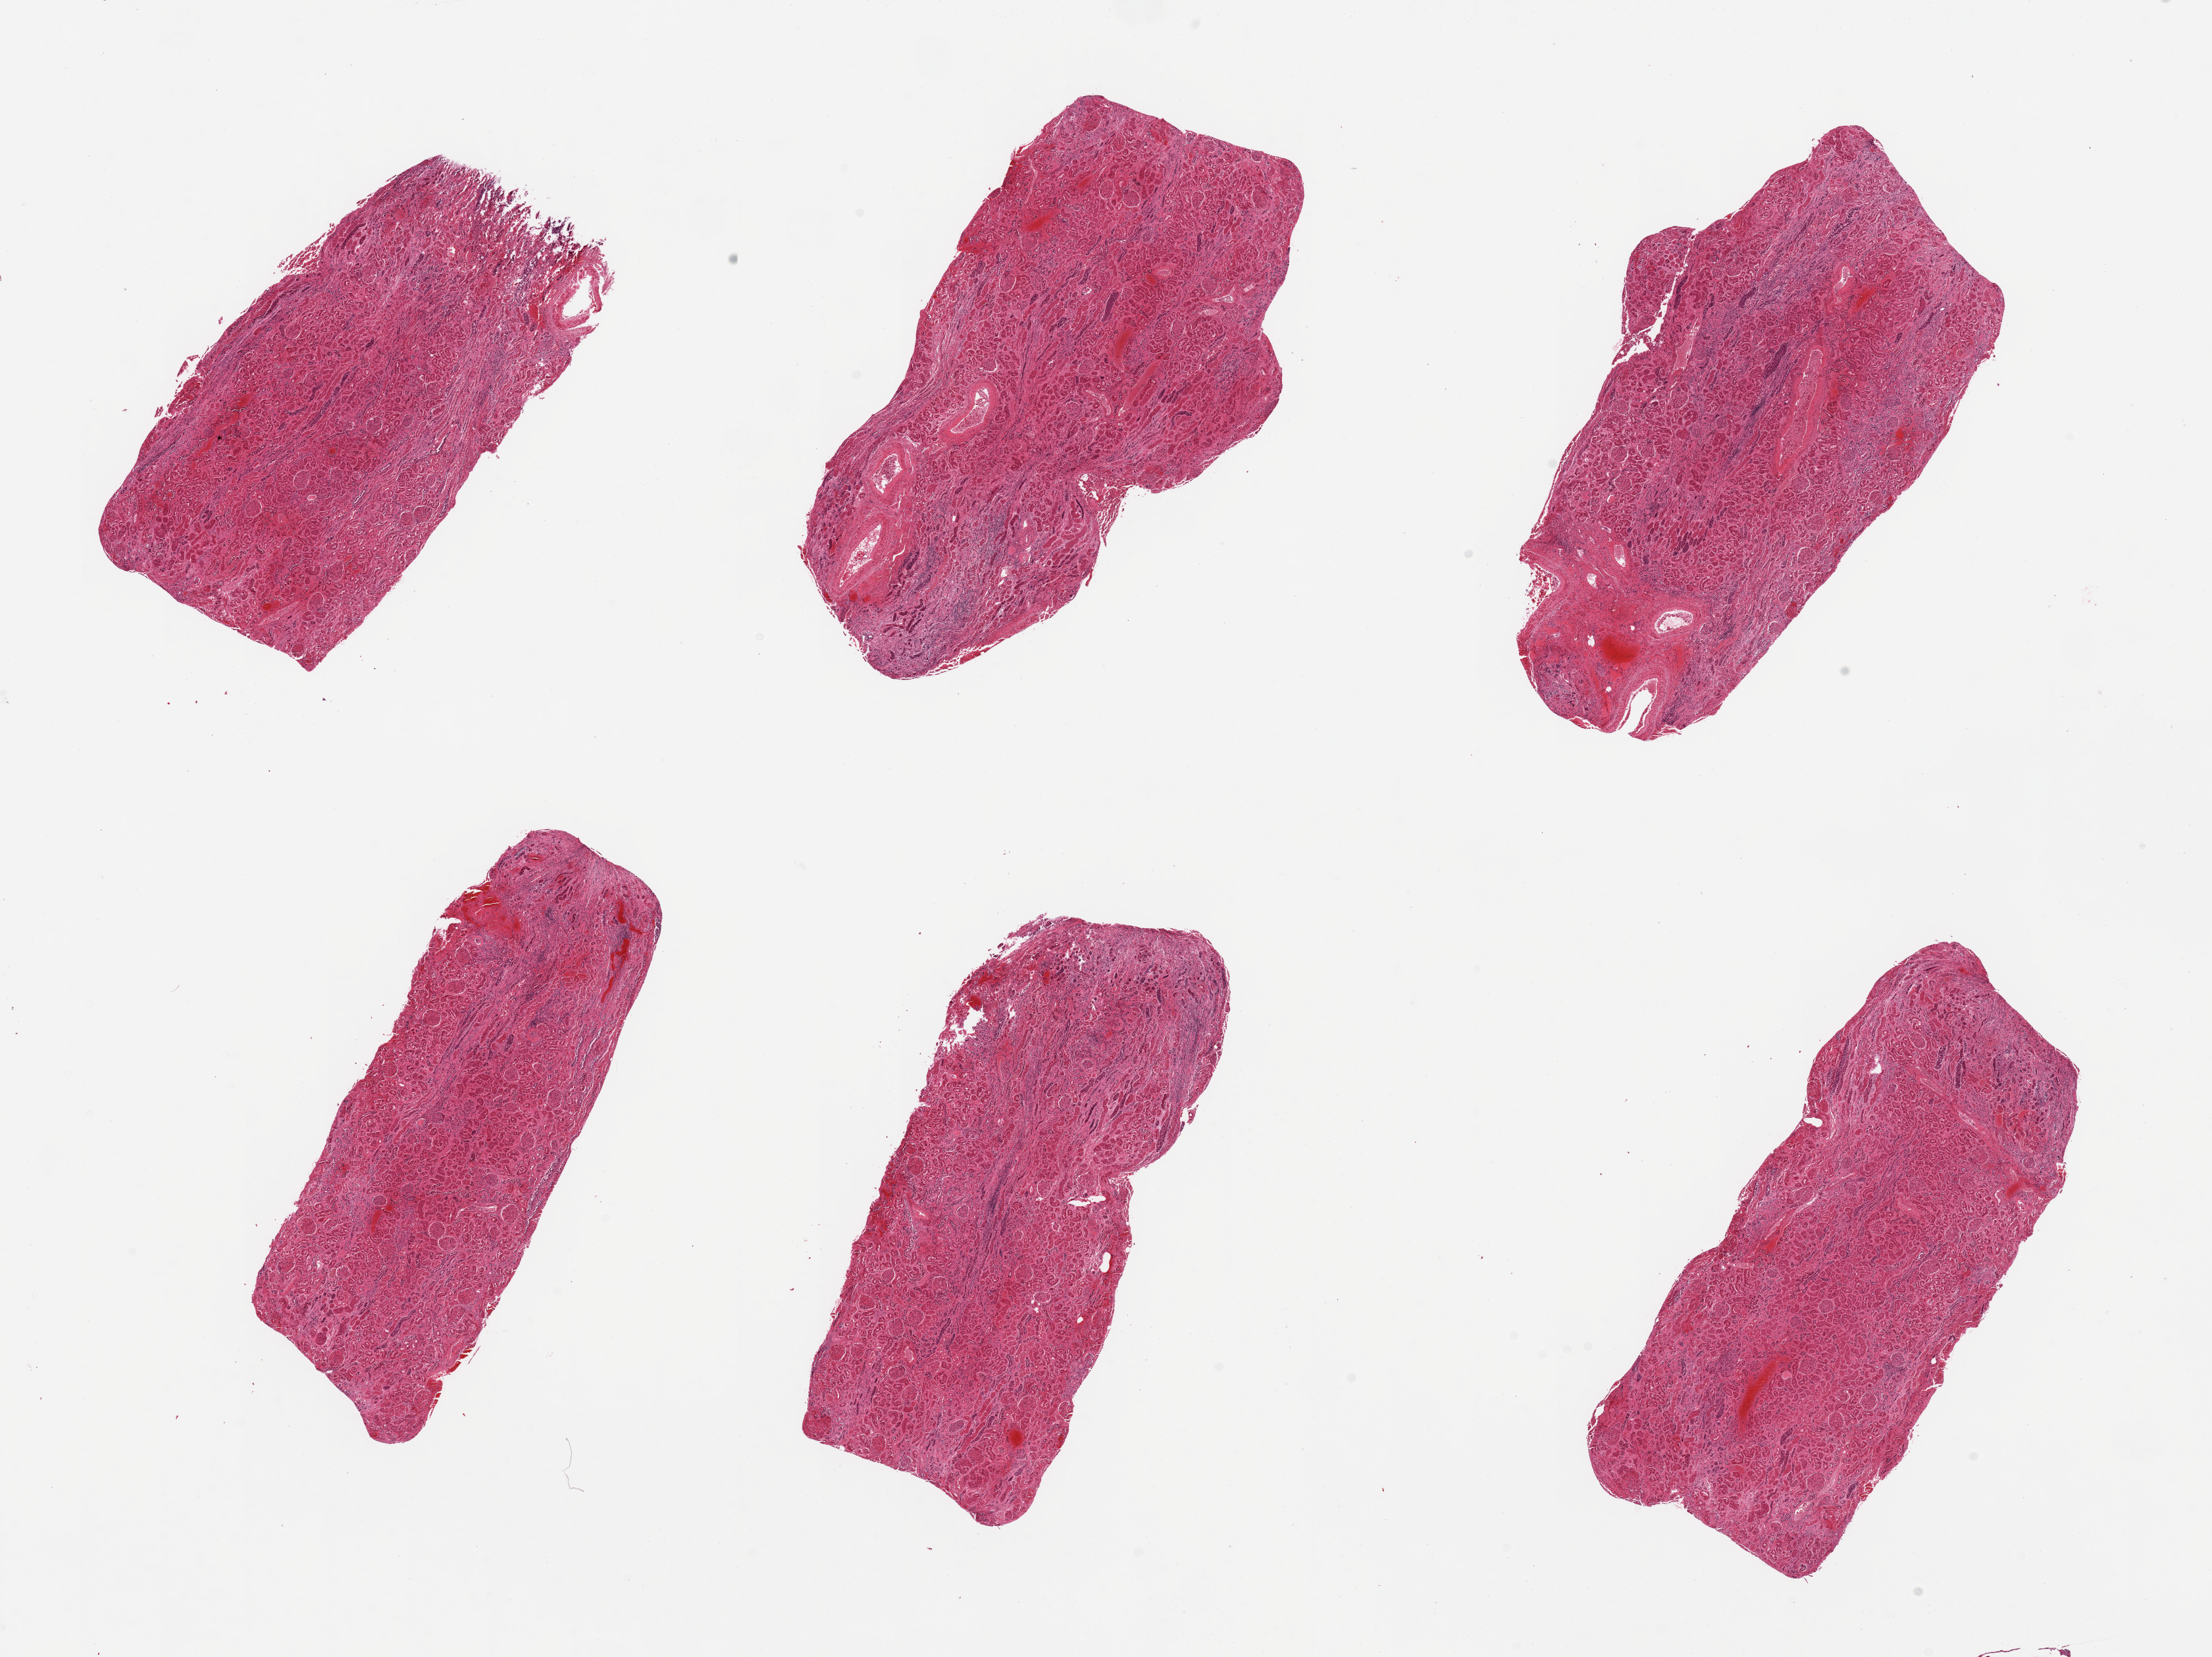
Digitized H&E-stained section, brightfield — whole scanned area (about 26.6 x 19.9 mm, acquisition: 20x scan) shown as a low-resolution overview. PAXgene-fixed, paraffin-embedded tissue. Target tissue: renal cortex. Donor tissue sample. Donor sex: male.
Review note (as recorded): 6 pieces; no sign of chronic disease.